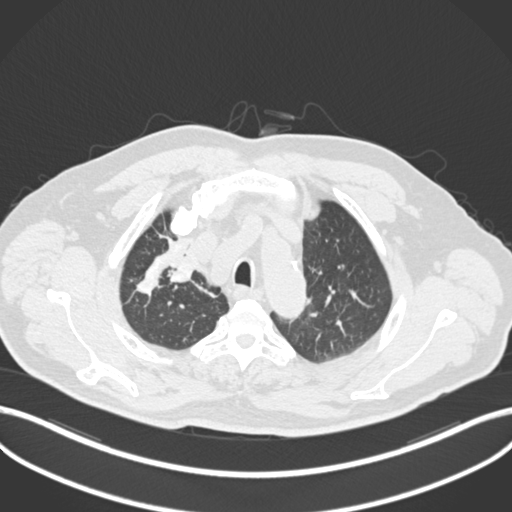
Chest CT, one axial slice. Position 165 of 255 along the scan axis. Reconstruction kernel B30f. 120 kVp. Lung window (W 1500 / L -600 HU). 1 mm slice thickness. 512 × 512 image matrix, field of view 400 × 400 mm. Patient: male, 60 years. From the clinical record (not read from this slice): clinical TNM (as recorded): T1b N1 M0.
Annotated regions visible in this slice (rectangle marked by the reading radiologist):
- lung tumour (recorded histology: squamous cell carcinoma): bounding box <168,252,205,287> (left, top, right, bottom; pixels)